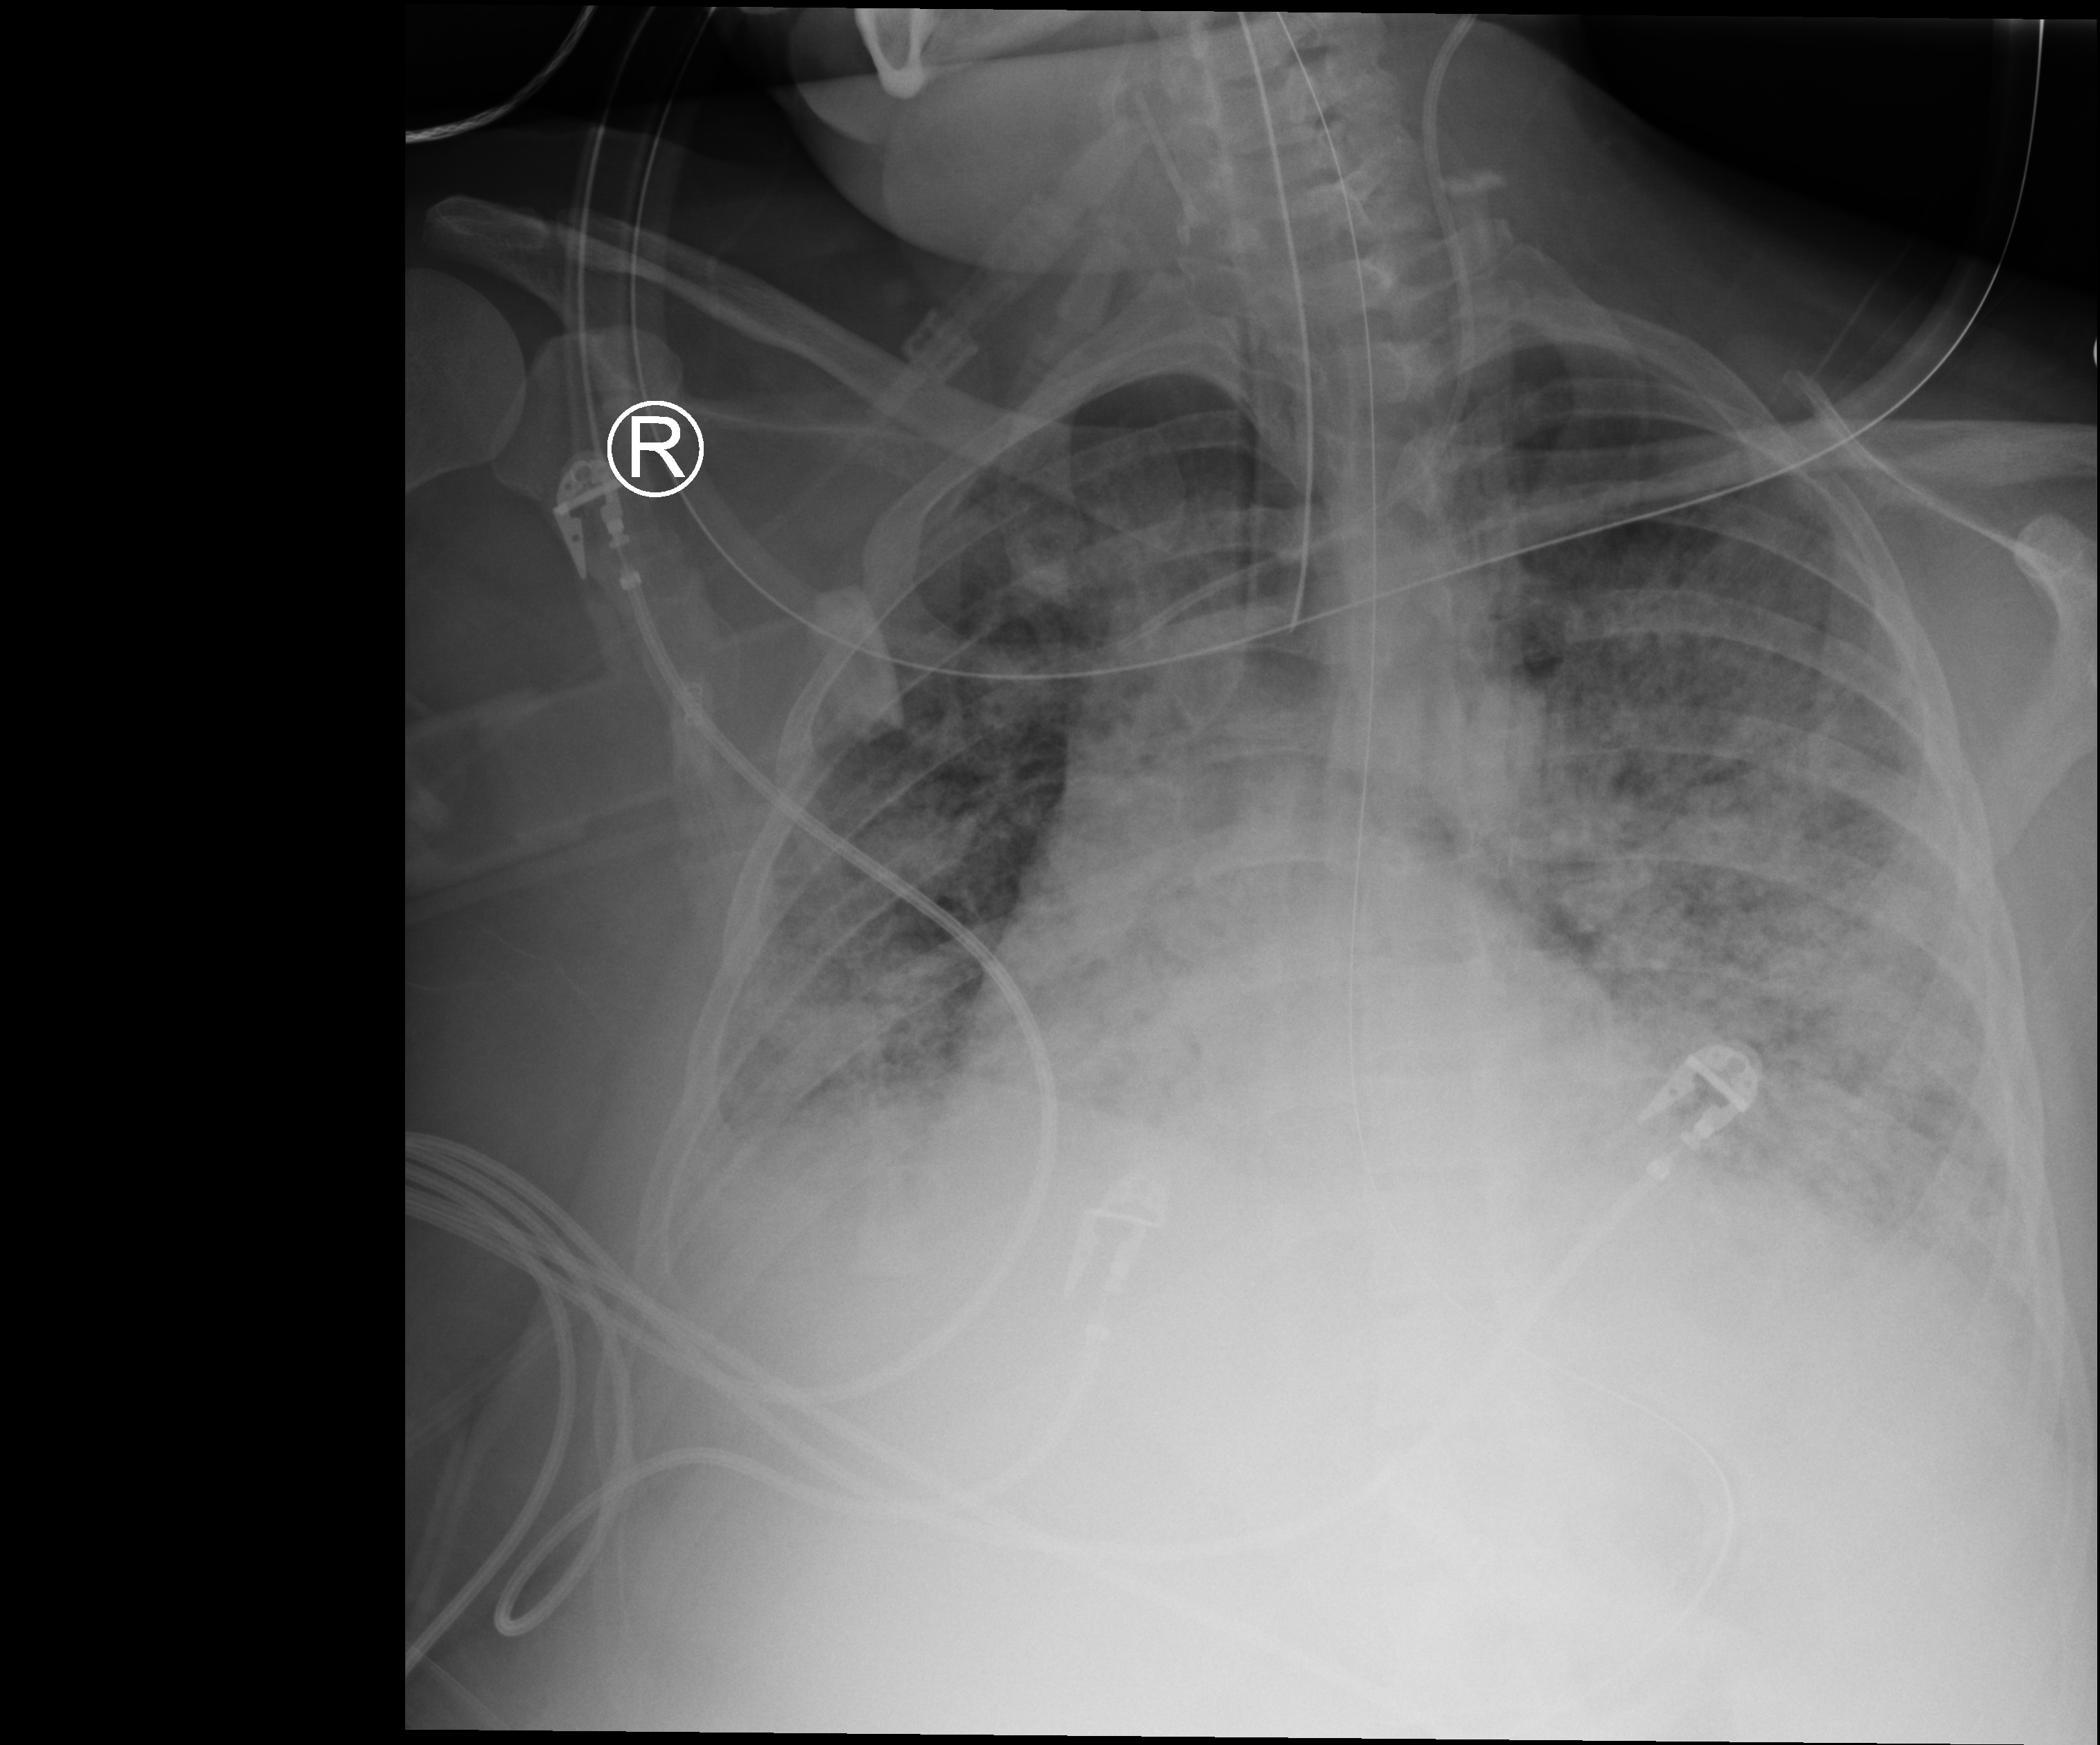
Portable chest radiograph, anteroposterior (AP) projection. Female patient hospitalised with COVID-19, age 18–59 years.
From the hospital-stay record, not from the radiograph (when in the stay this image was taken is not recorded): mechanically ventilated during this hospital stay: yes.